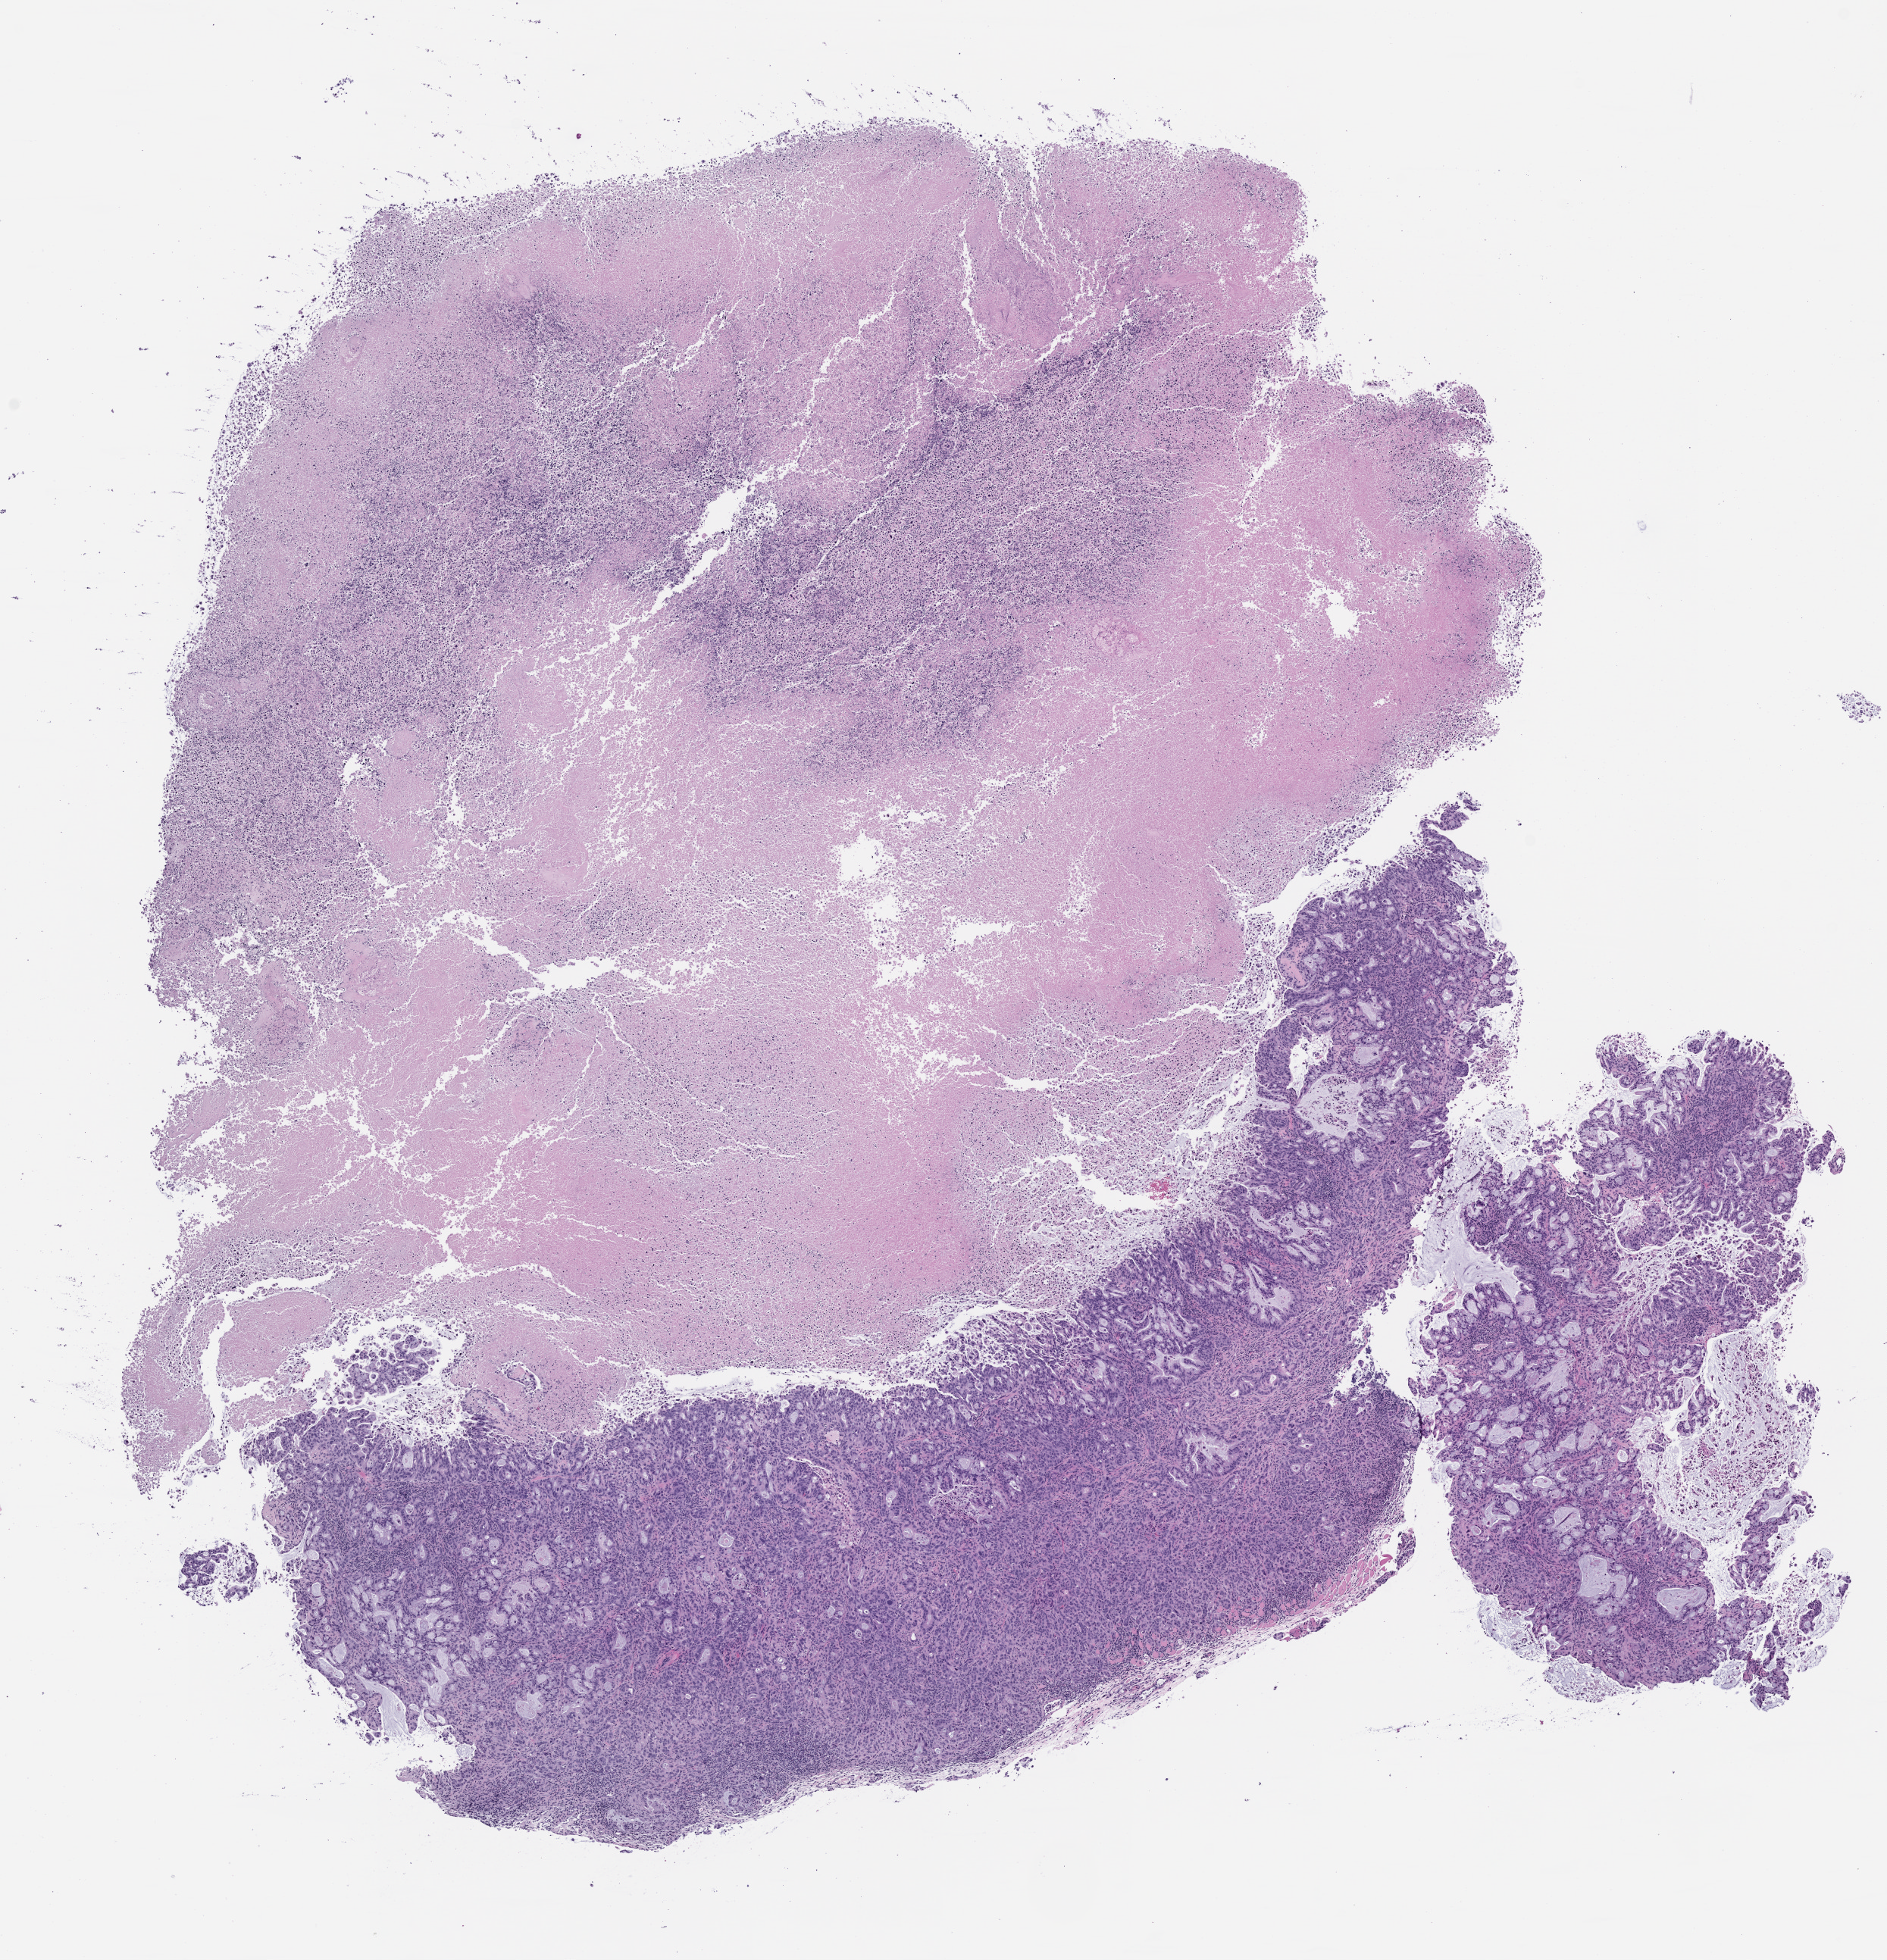
Hematoxylin and eosin (H&E) whole-slide image of a patient-derived xenograft (PDX) tumor grown in a mouse, passage 3 — a low-resolution overview of the entire scanned area, about 10.0 x 10.4 mm; FFPE section; originating tumor site category: pancreas.
- originating patient diagnosis: Pancreatic Adenocarcinoma